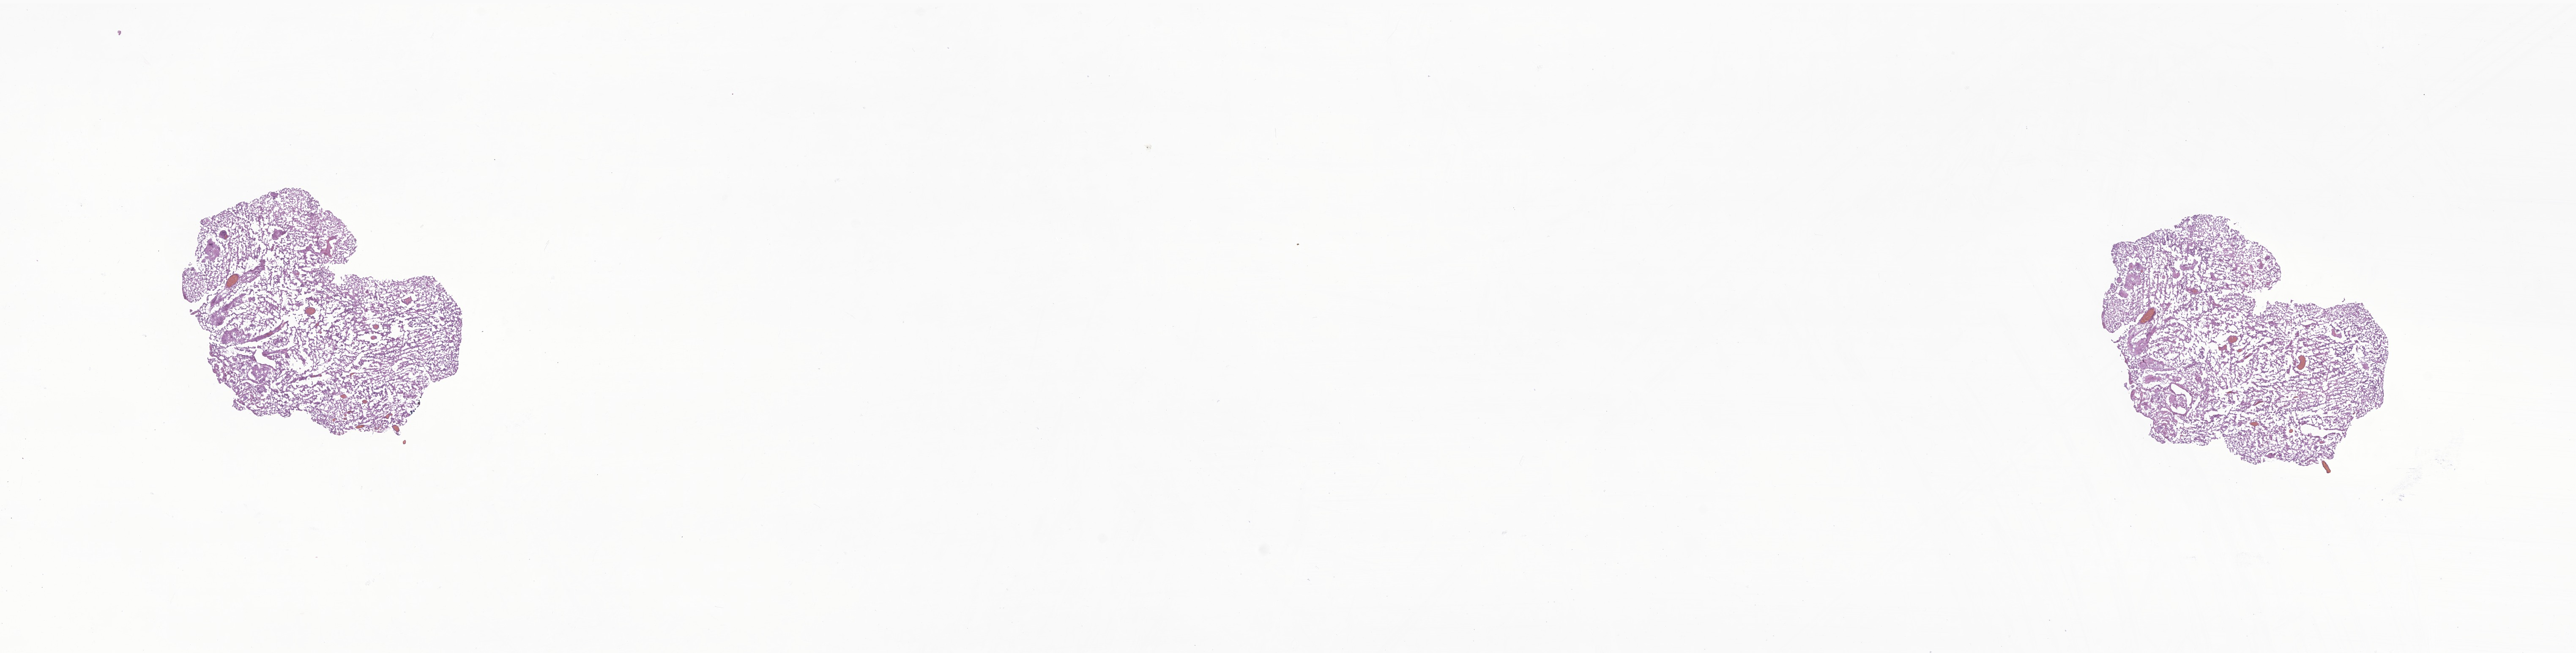
Digitized haematoxylin and eosin-stained section of tumor tissue from the temporal lobe, low-resolution overview of the scanned area, about 25.7 x 6.5 mm. Frozen section. Patient: female, age 96 months (8 years).
Diagnosis: Astrocytoma, NOS.